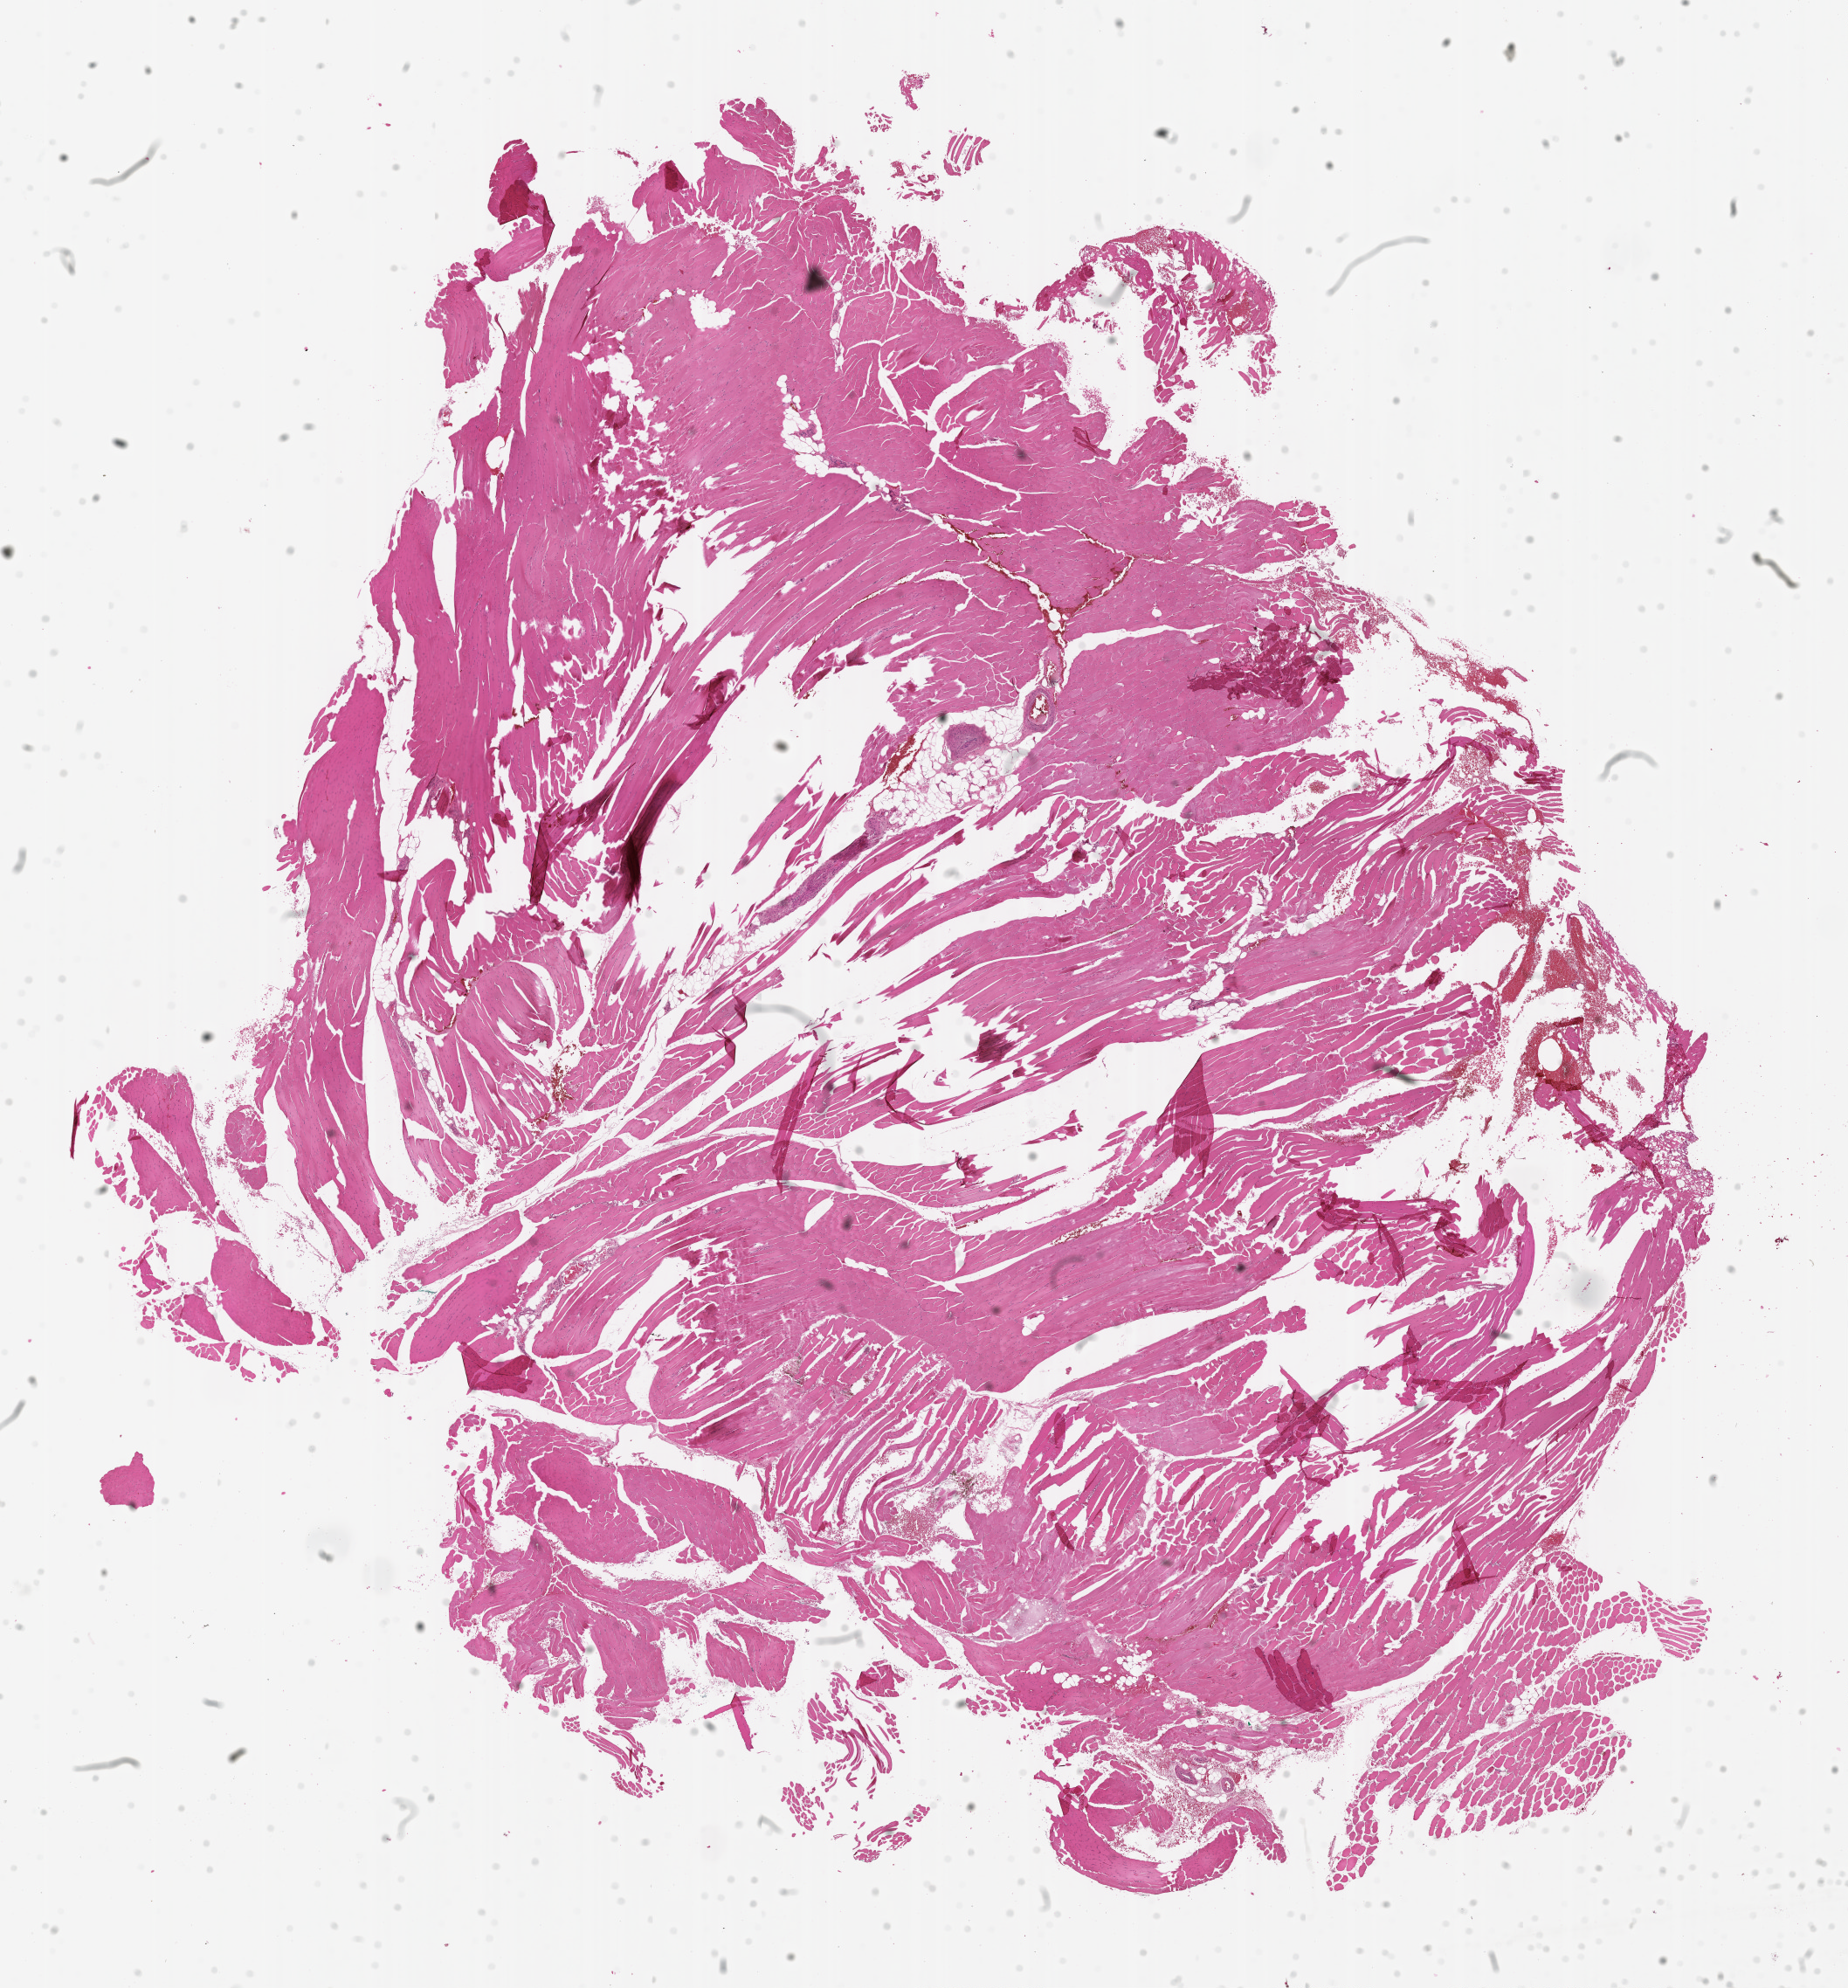
H&E whole-slide image, a low-resolution overview of the entire scanned area, about 17.0 x 18.3 mm (from a 20x scan).
Patient diagnosis (cohort enrolment): sarcoma (site not recorded at cohort level).